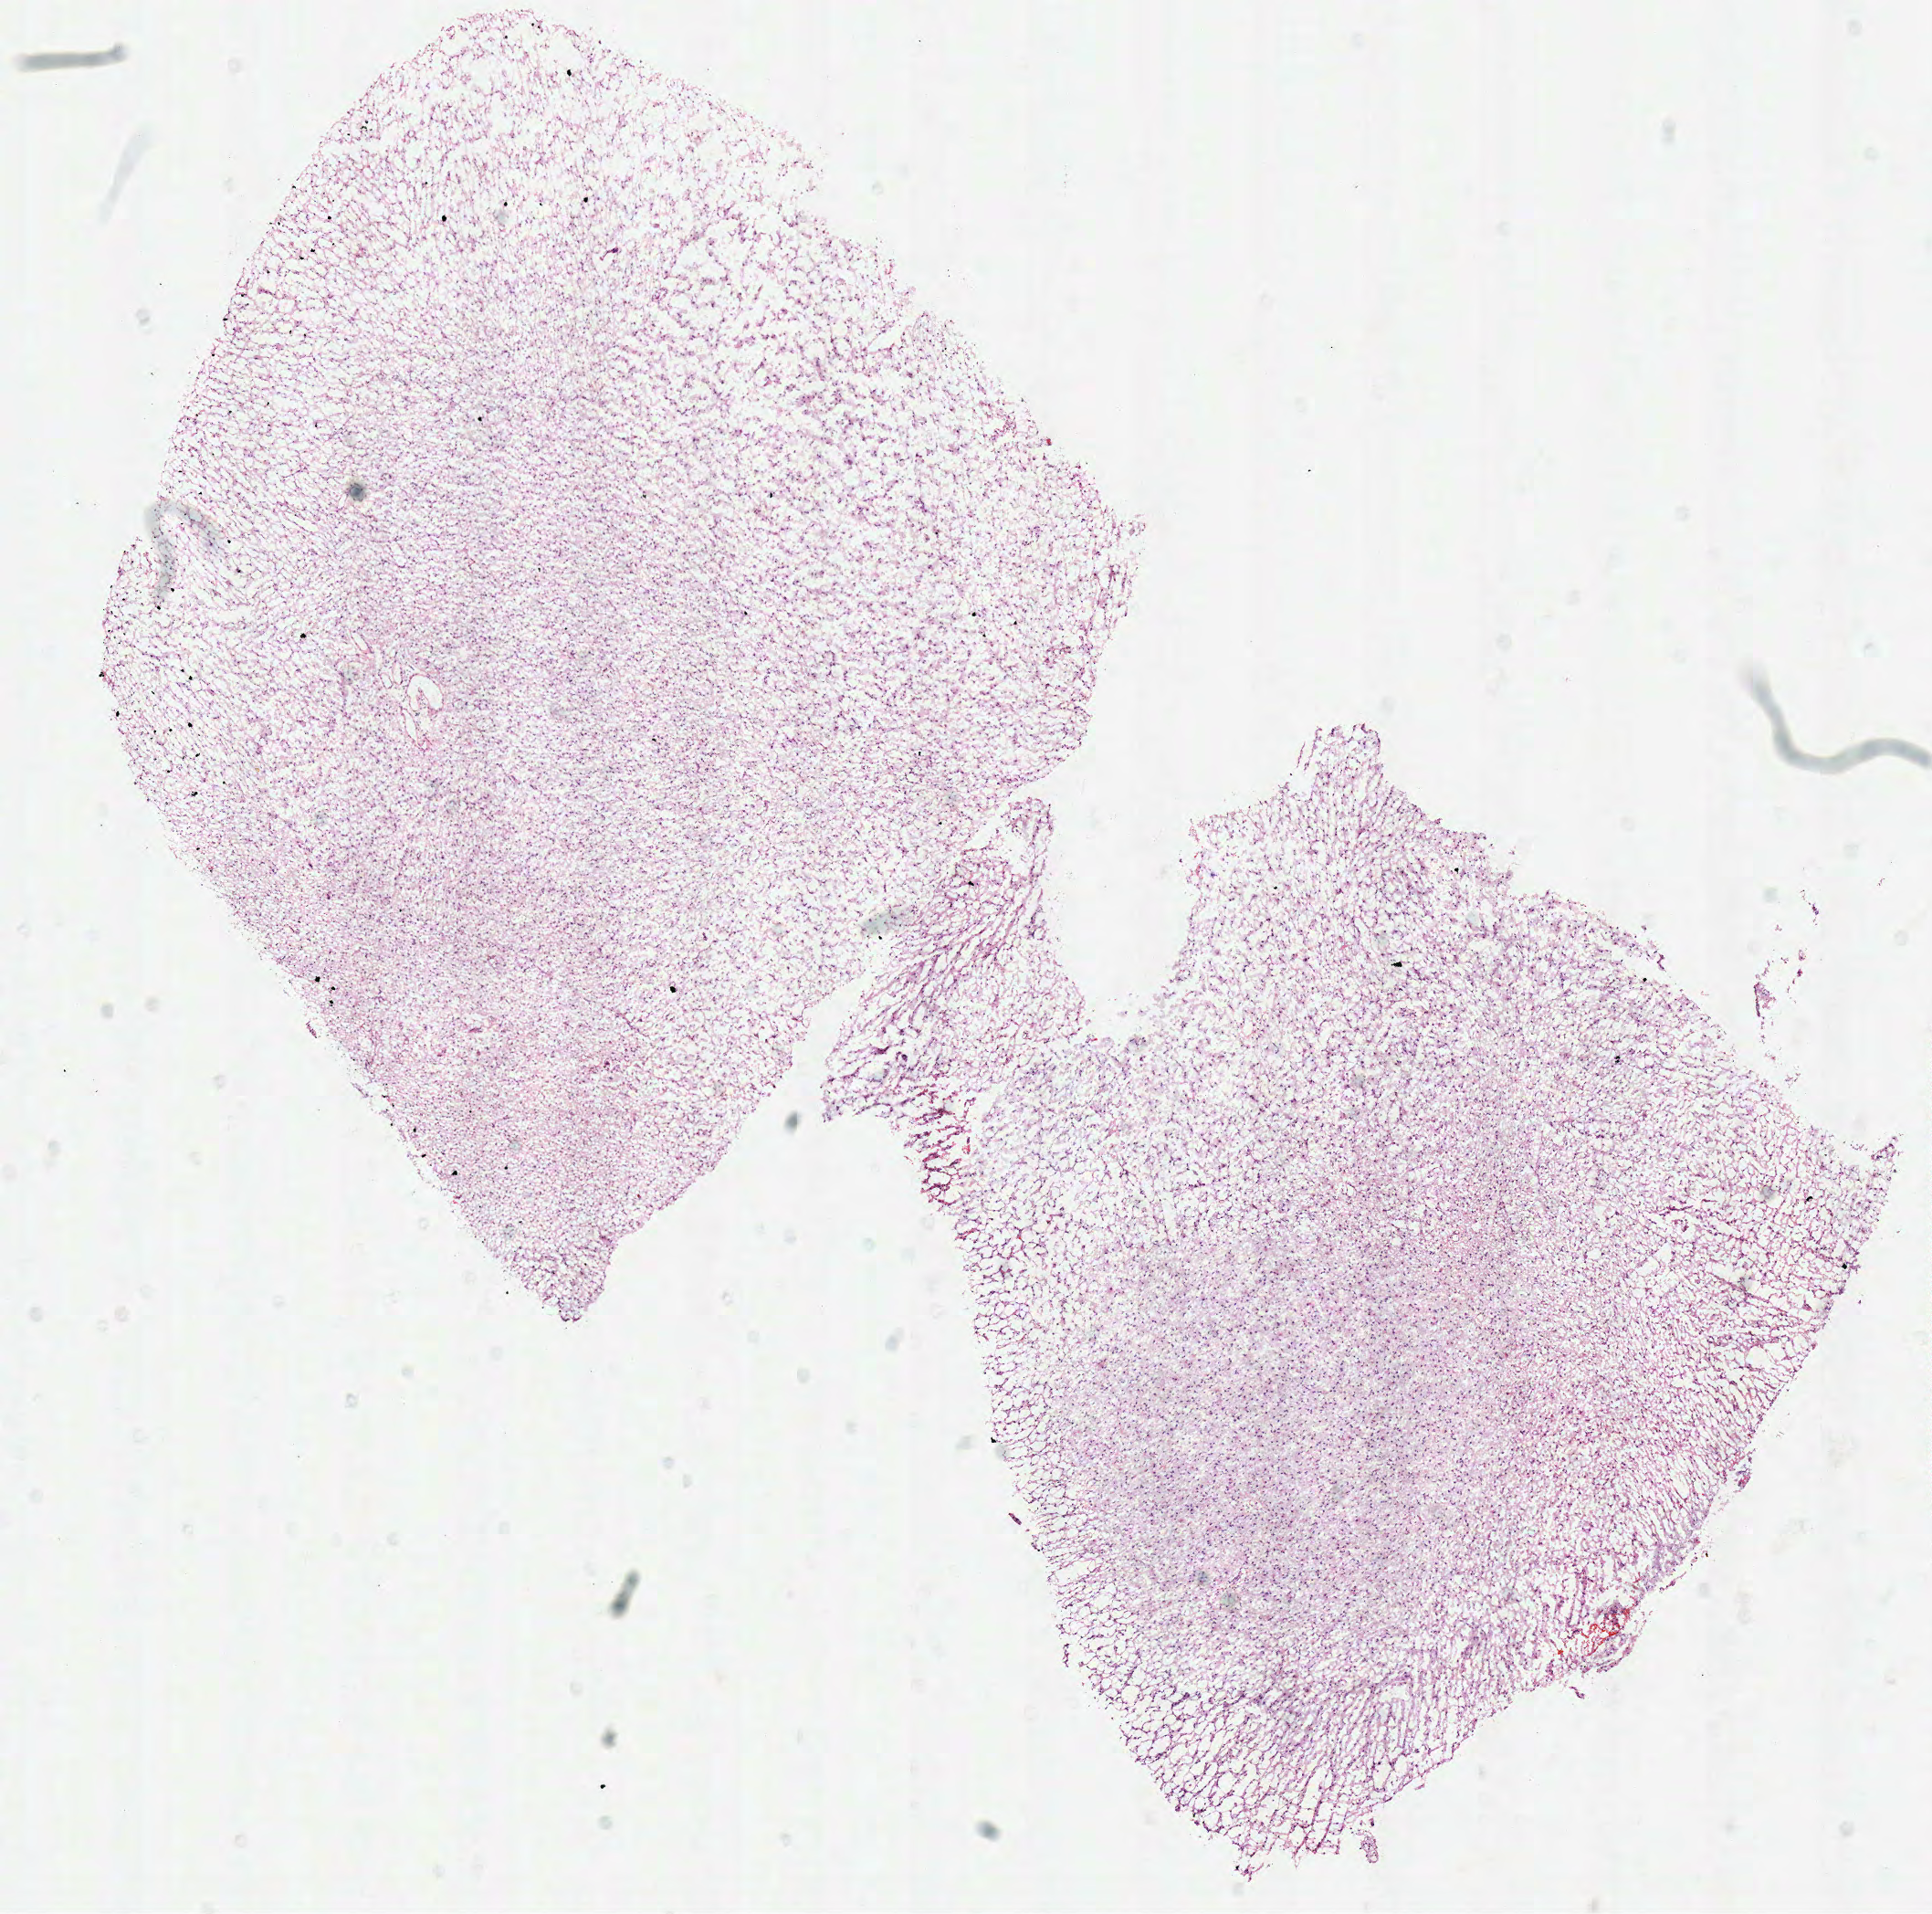
Hematoxylin and eosin (H&E) stained whole-slide image, shown as a low-resolution overview of the whole scanned area (about 8.3 x 8.2 mm, slide scanned at 40x), frozen section from the top of the tissue portion, brain, primary tumour sample. Patient: male, age at initial diagnosis 70 years. Histologic grade: G2 (moderately differentiated). Slide review estimates, as recorded: tumour cells 100%, tumour nuclei 75%, normal cells 0%, stromal cells 0%, necrosis 0%.
Histologic diagnosis: Oligodendroglioma, NOS (cerebrum). Laterality: left.